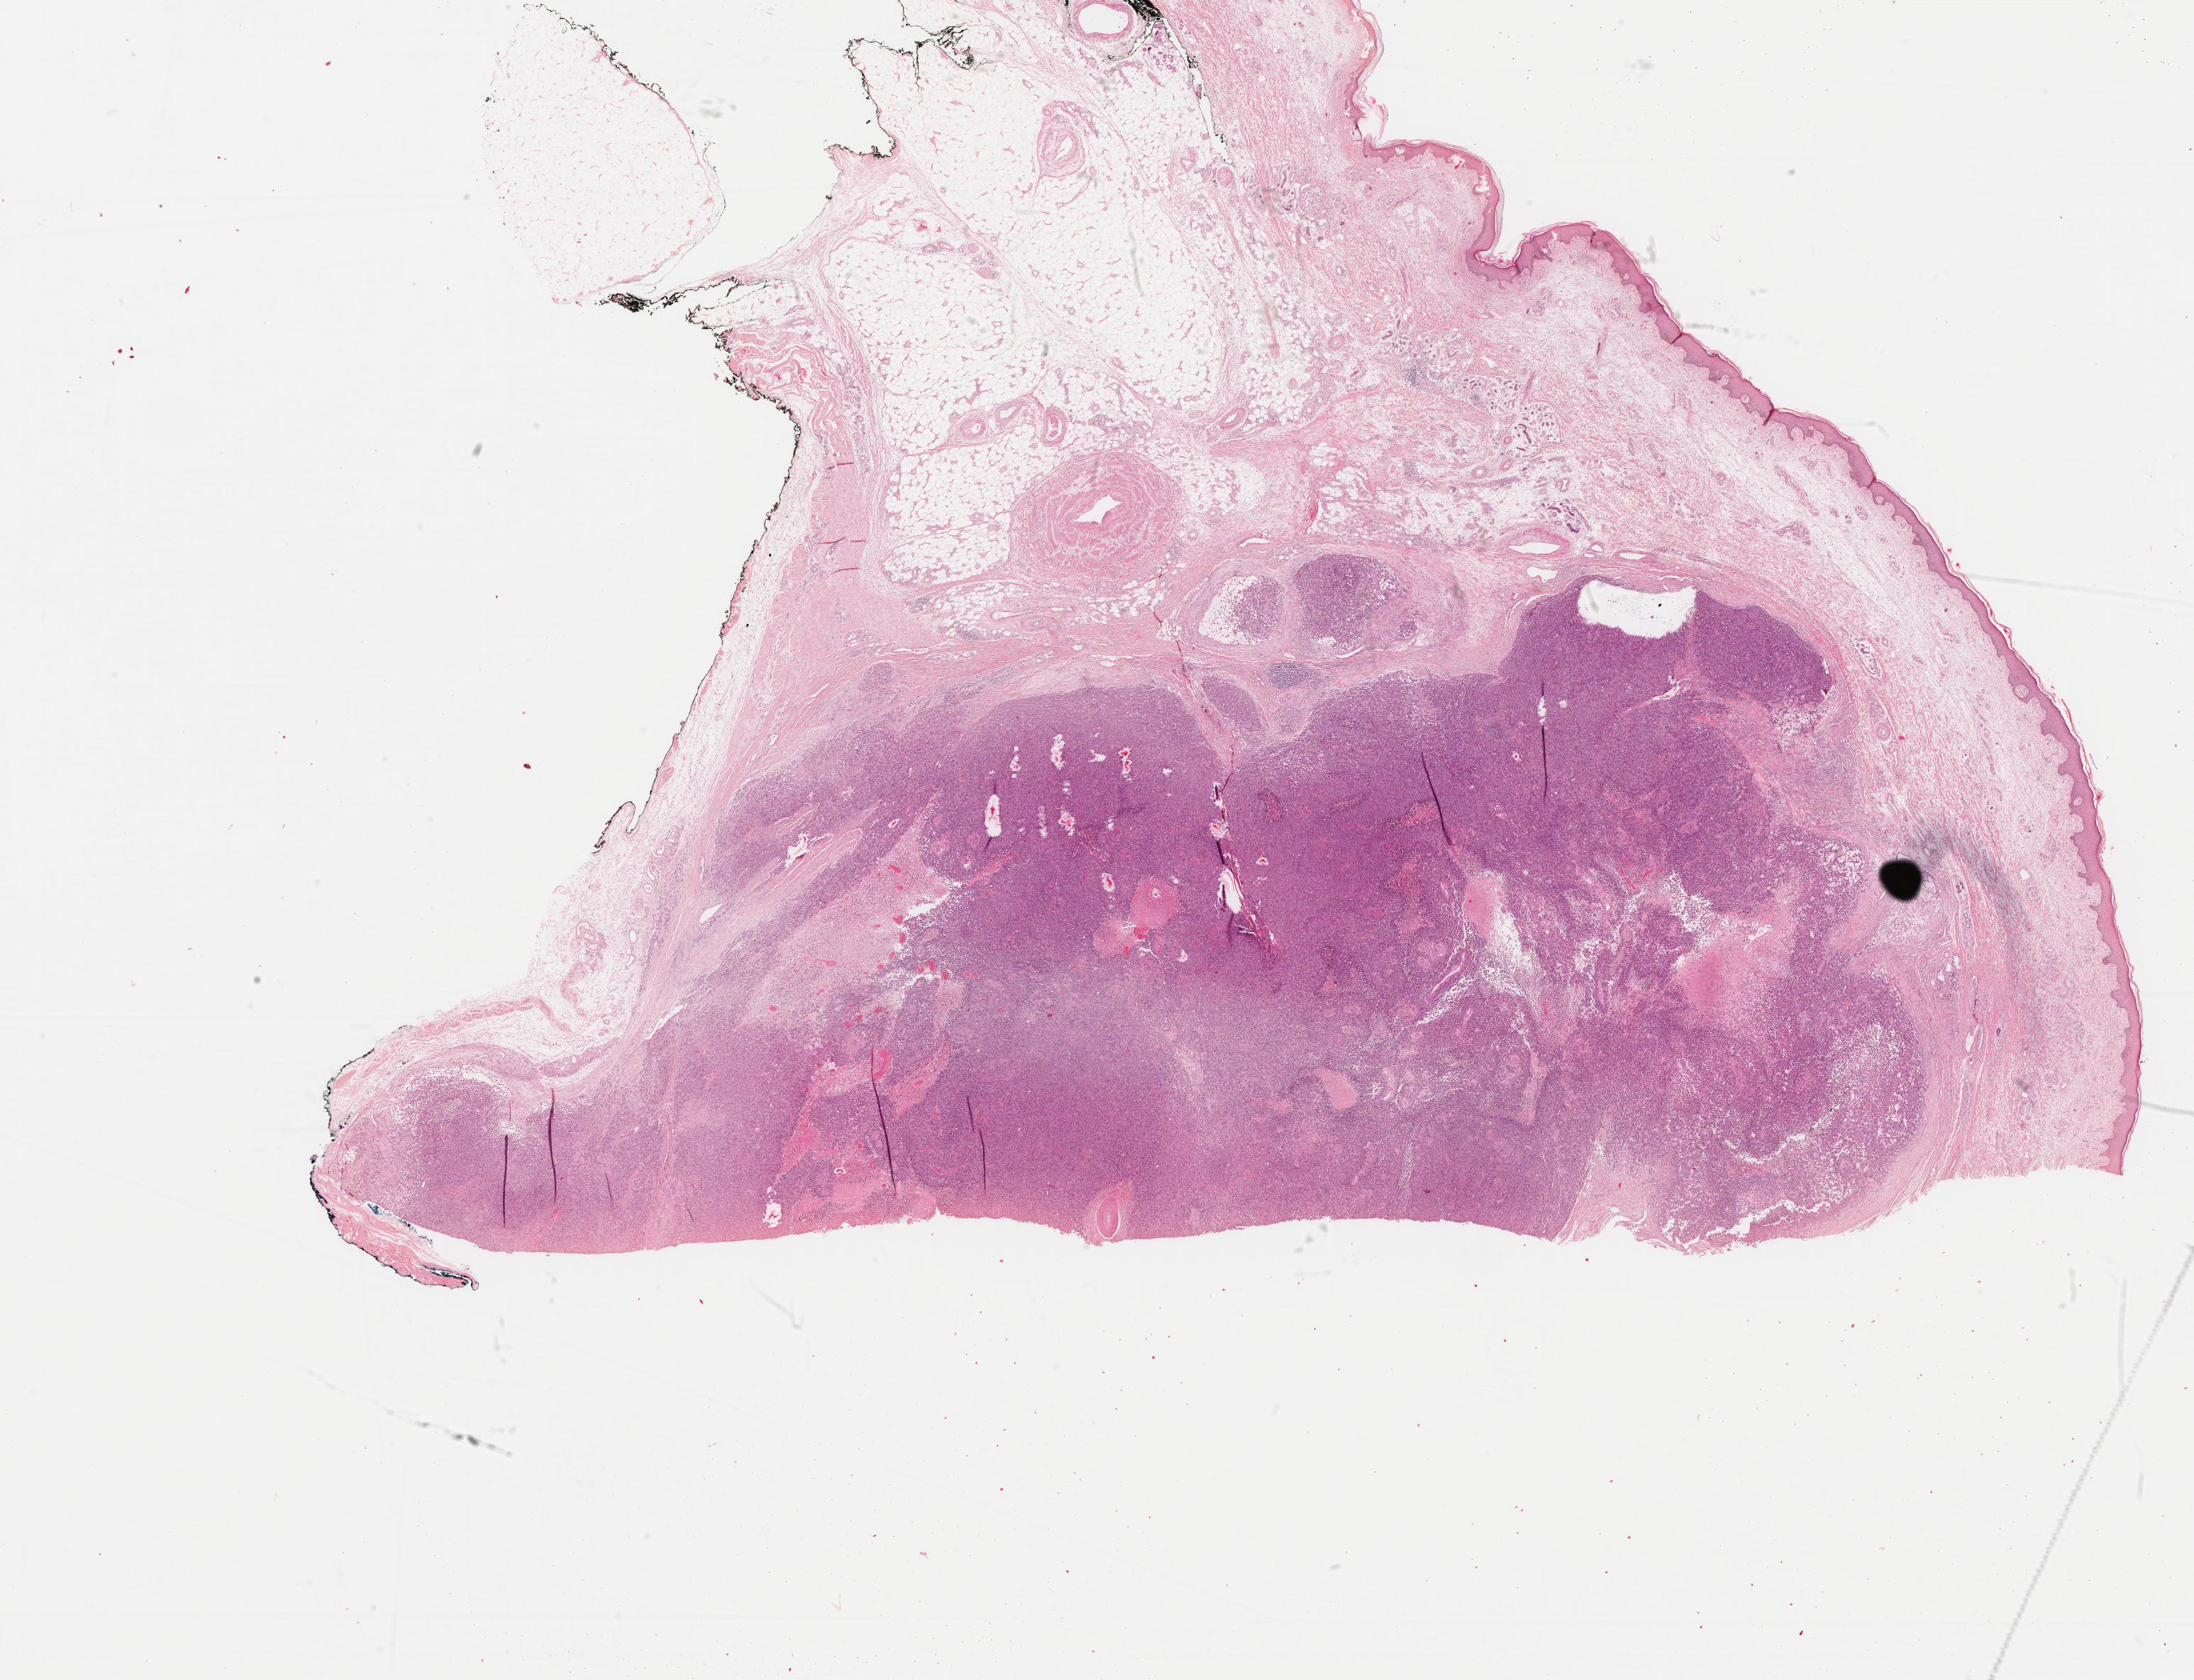
H&E-stained whole-slide image — a low-resolution overview of the entire scanned area, about 24.6 x 18.8 mm (from a 40x scan); formalin-fixed paraffin-embedded (FFPE) diagnostic section; primary tumour sample from the skin. Female patient; age at initial diagnosis 66 years.
Diagnosis: Amelanotic melanoma.